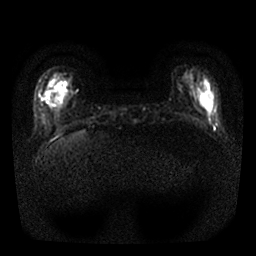
Breast MRI, one axial slice; slice 5 of 25 in the series (ordered by position); diffusion-weighted series; image 2 of 4 stored at this slice position (different b-values; order by instance number); 1.5 T; 4 mm slice thickness; 256 × 256 image matrix. Female patient.
Annotated regions visible in this slice (expert manual segmentation):
- tumour on diffusion-weighted imaging: bounding box (x1, y1, x2, y2) in pixels: (43, 96, 48, 101)